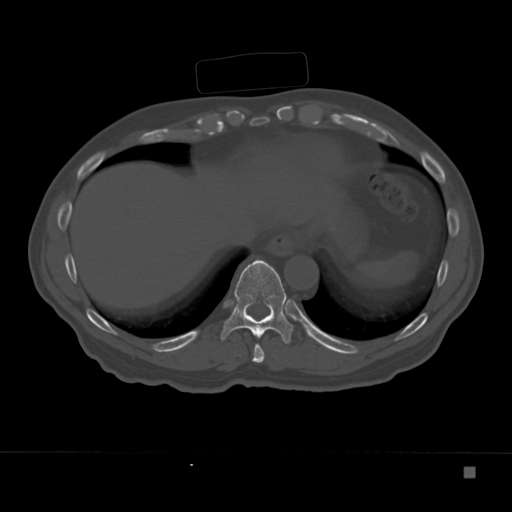
CT including the spine, one axial slice; slice 174 of 332 in the series (ordered by position); 120 kVp; bone window (W 1800 / L 400 HU); 1.5 mm slice thickness; 512 × 512 image matrix, field of view 389 × 389 mm. Male patient, age 72 years. Case-level facts recorded for this patient, not image findings: primary cancer: skeletal.
Structures marked on this image (semi-automatically segmented with operator editing):
- T10 vertebra: bounding box (x1, y1, x2, y2) in pixels: (220, 260, 294, 344)
- T9 vertebra: (252, 344, 265, 363)